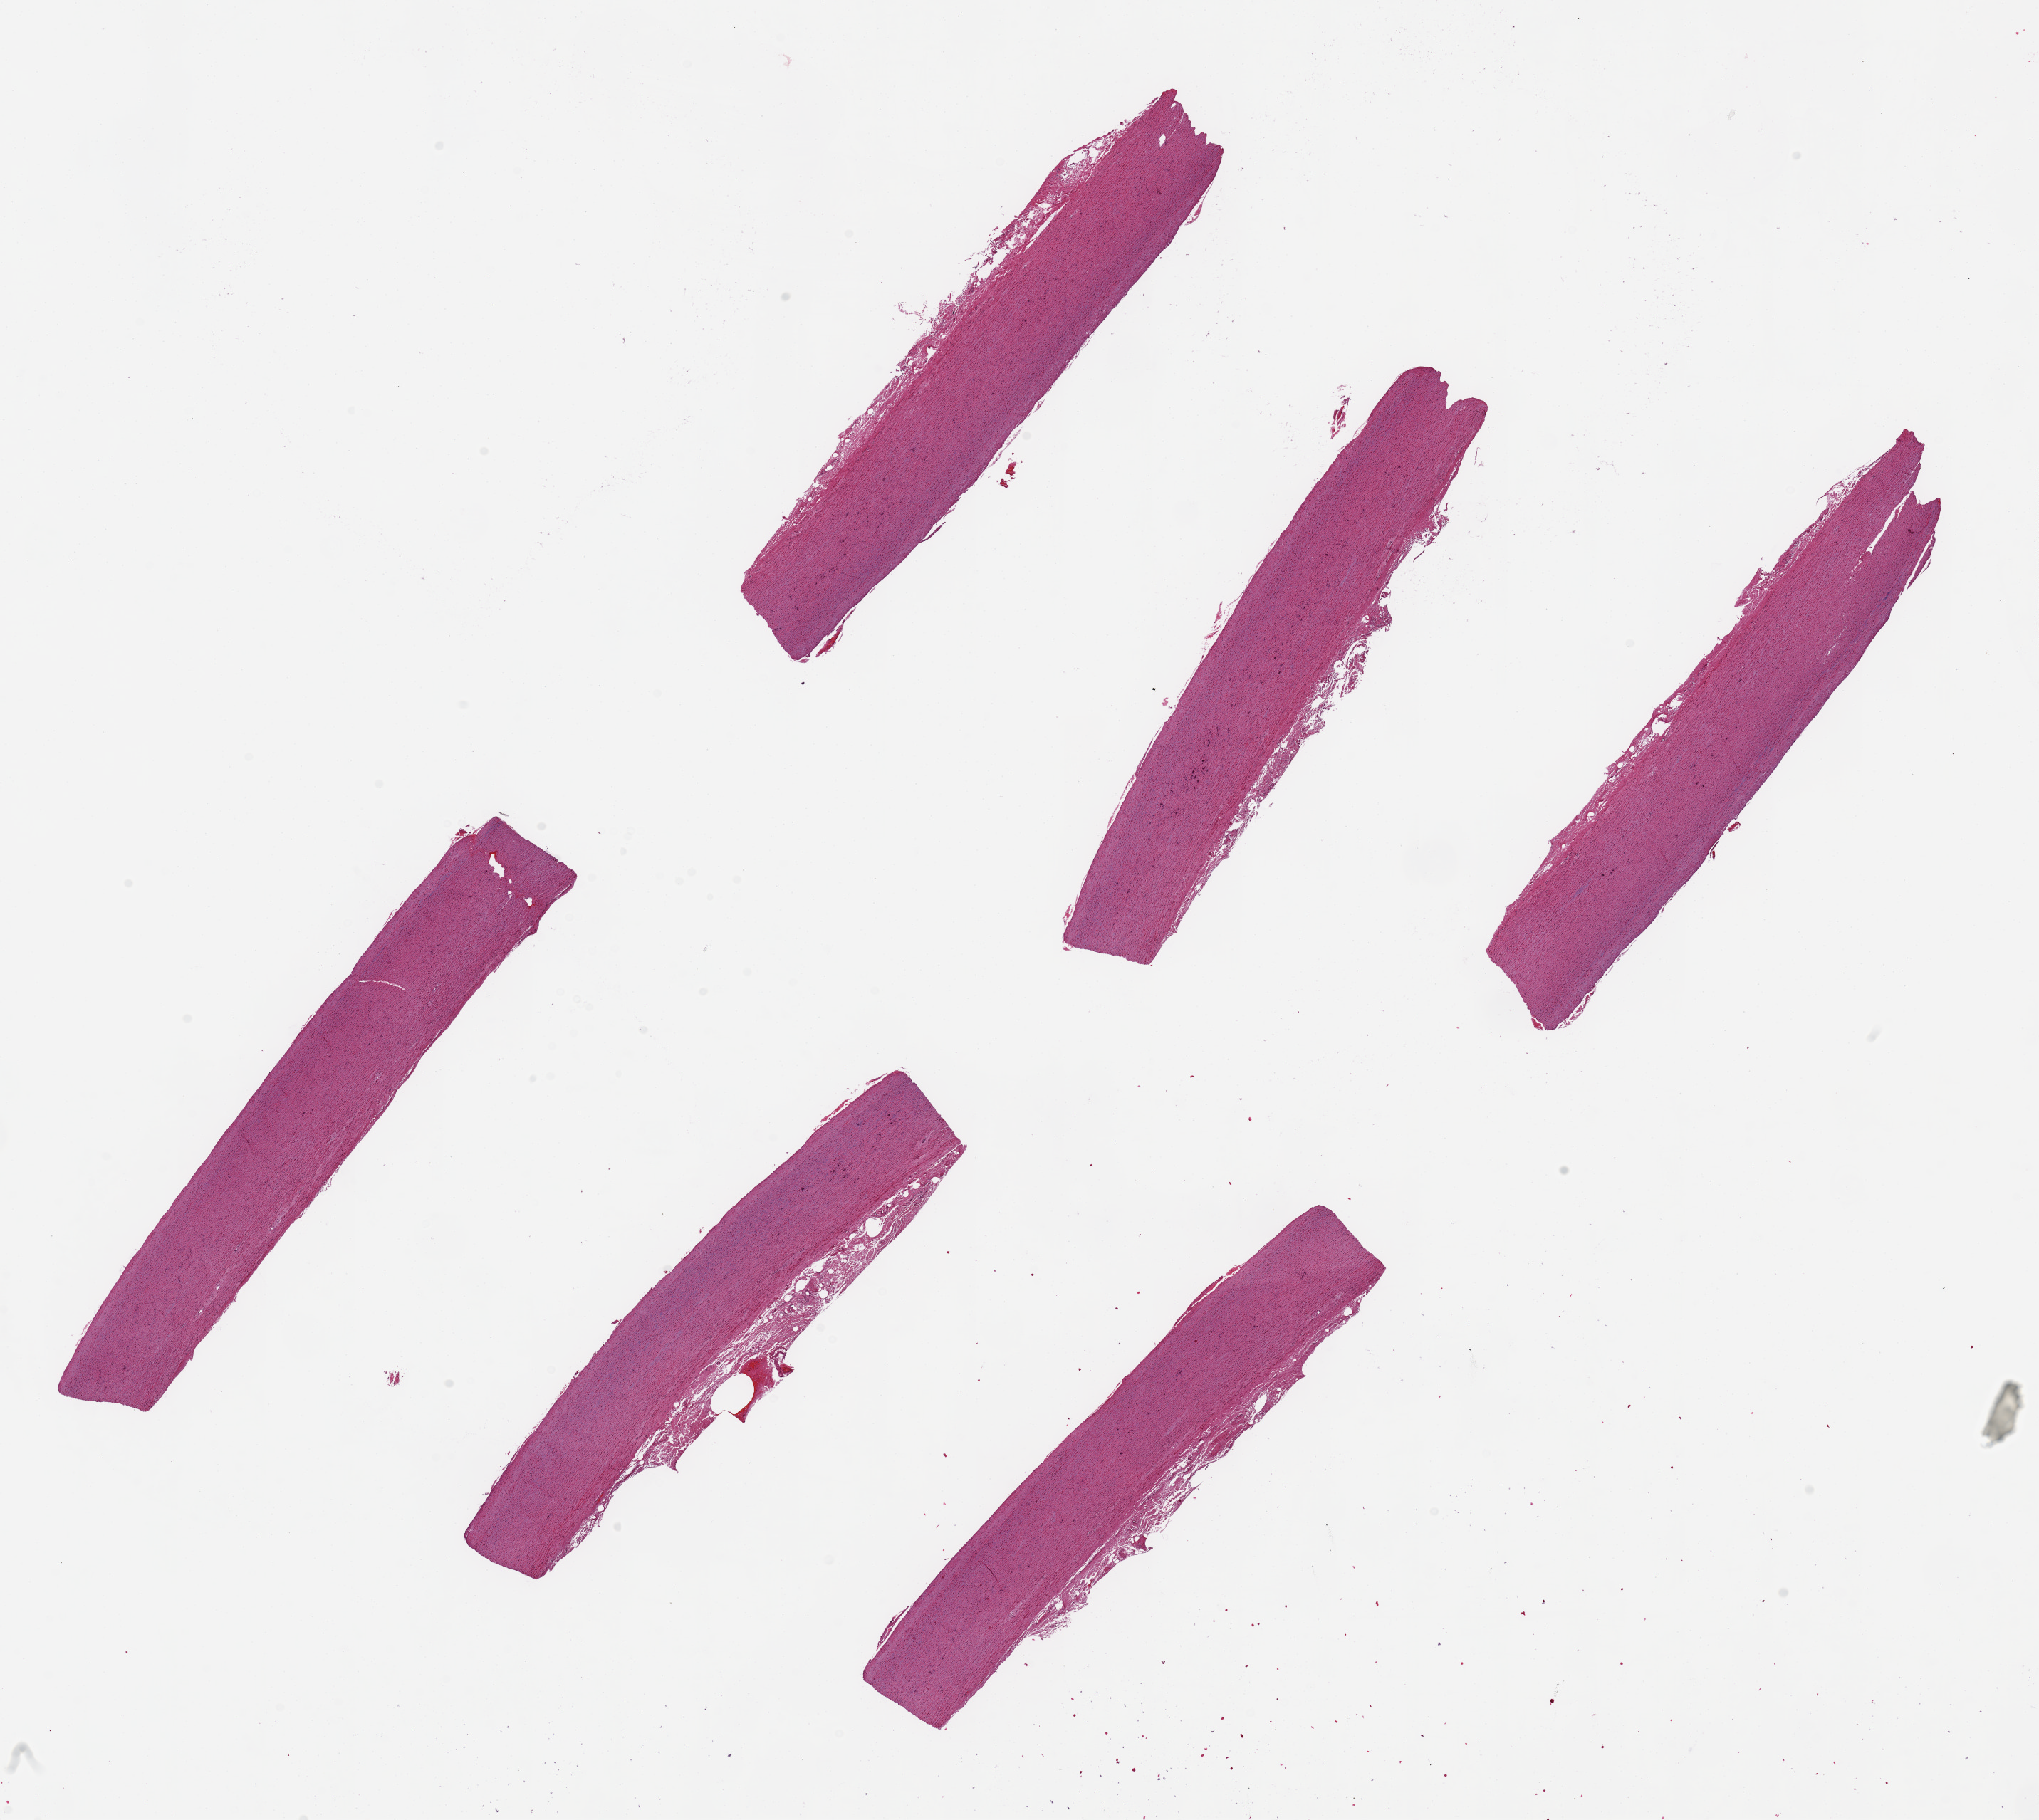
Hematoxylin and eosin (H&E) whole-slide image, a low-resolution overview of the entire scanned area, about 22.6 x 20.2 mm. PAXgene-fixed, paraffin-embedded tissue. Section of aorta (target tissue). Tissue donor sample.
Review note (as recorded): 6 pieces, ~7.5x1.2 mm.